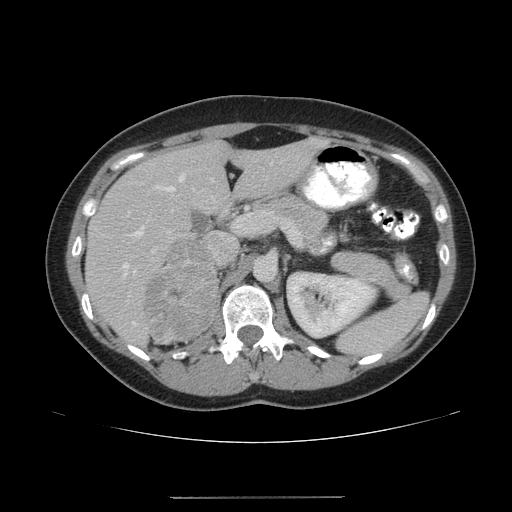
Contrast-enhanced abdominal CT, one axial slice; slice 109 of 161 in the series (ordered by position); reconstruction kernel STANDARD; 120 kVp; intravenous contrast given; soft-tissue window (W 400 / L 40 HU); 3.75 mm slice thickness; 512 × 512 image matrix, field of view 380 × 380 mm. Female patient. From the clinical record (not read from this slice): diagnosis: adrenocortical carcinoma; tumour side: right adrenal; tumour size at pathology: 9 cm; Ki-67 index: 14 %; stage (as recorded): 3.
Structures marked on this image (semi-automatically segmented with operator editing):
- mass: bounding box <146,239,217,344> (left, top, right, bottom; pixels)